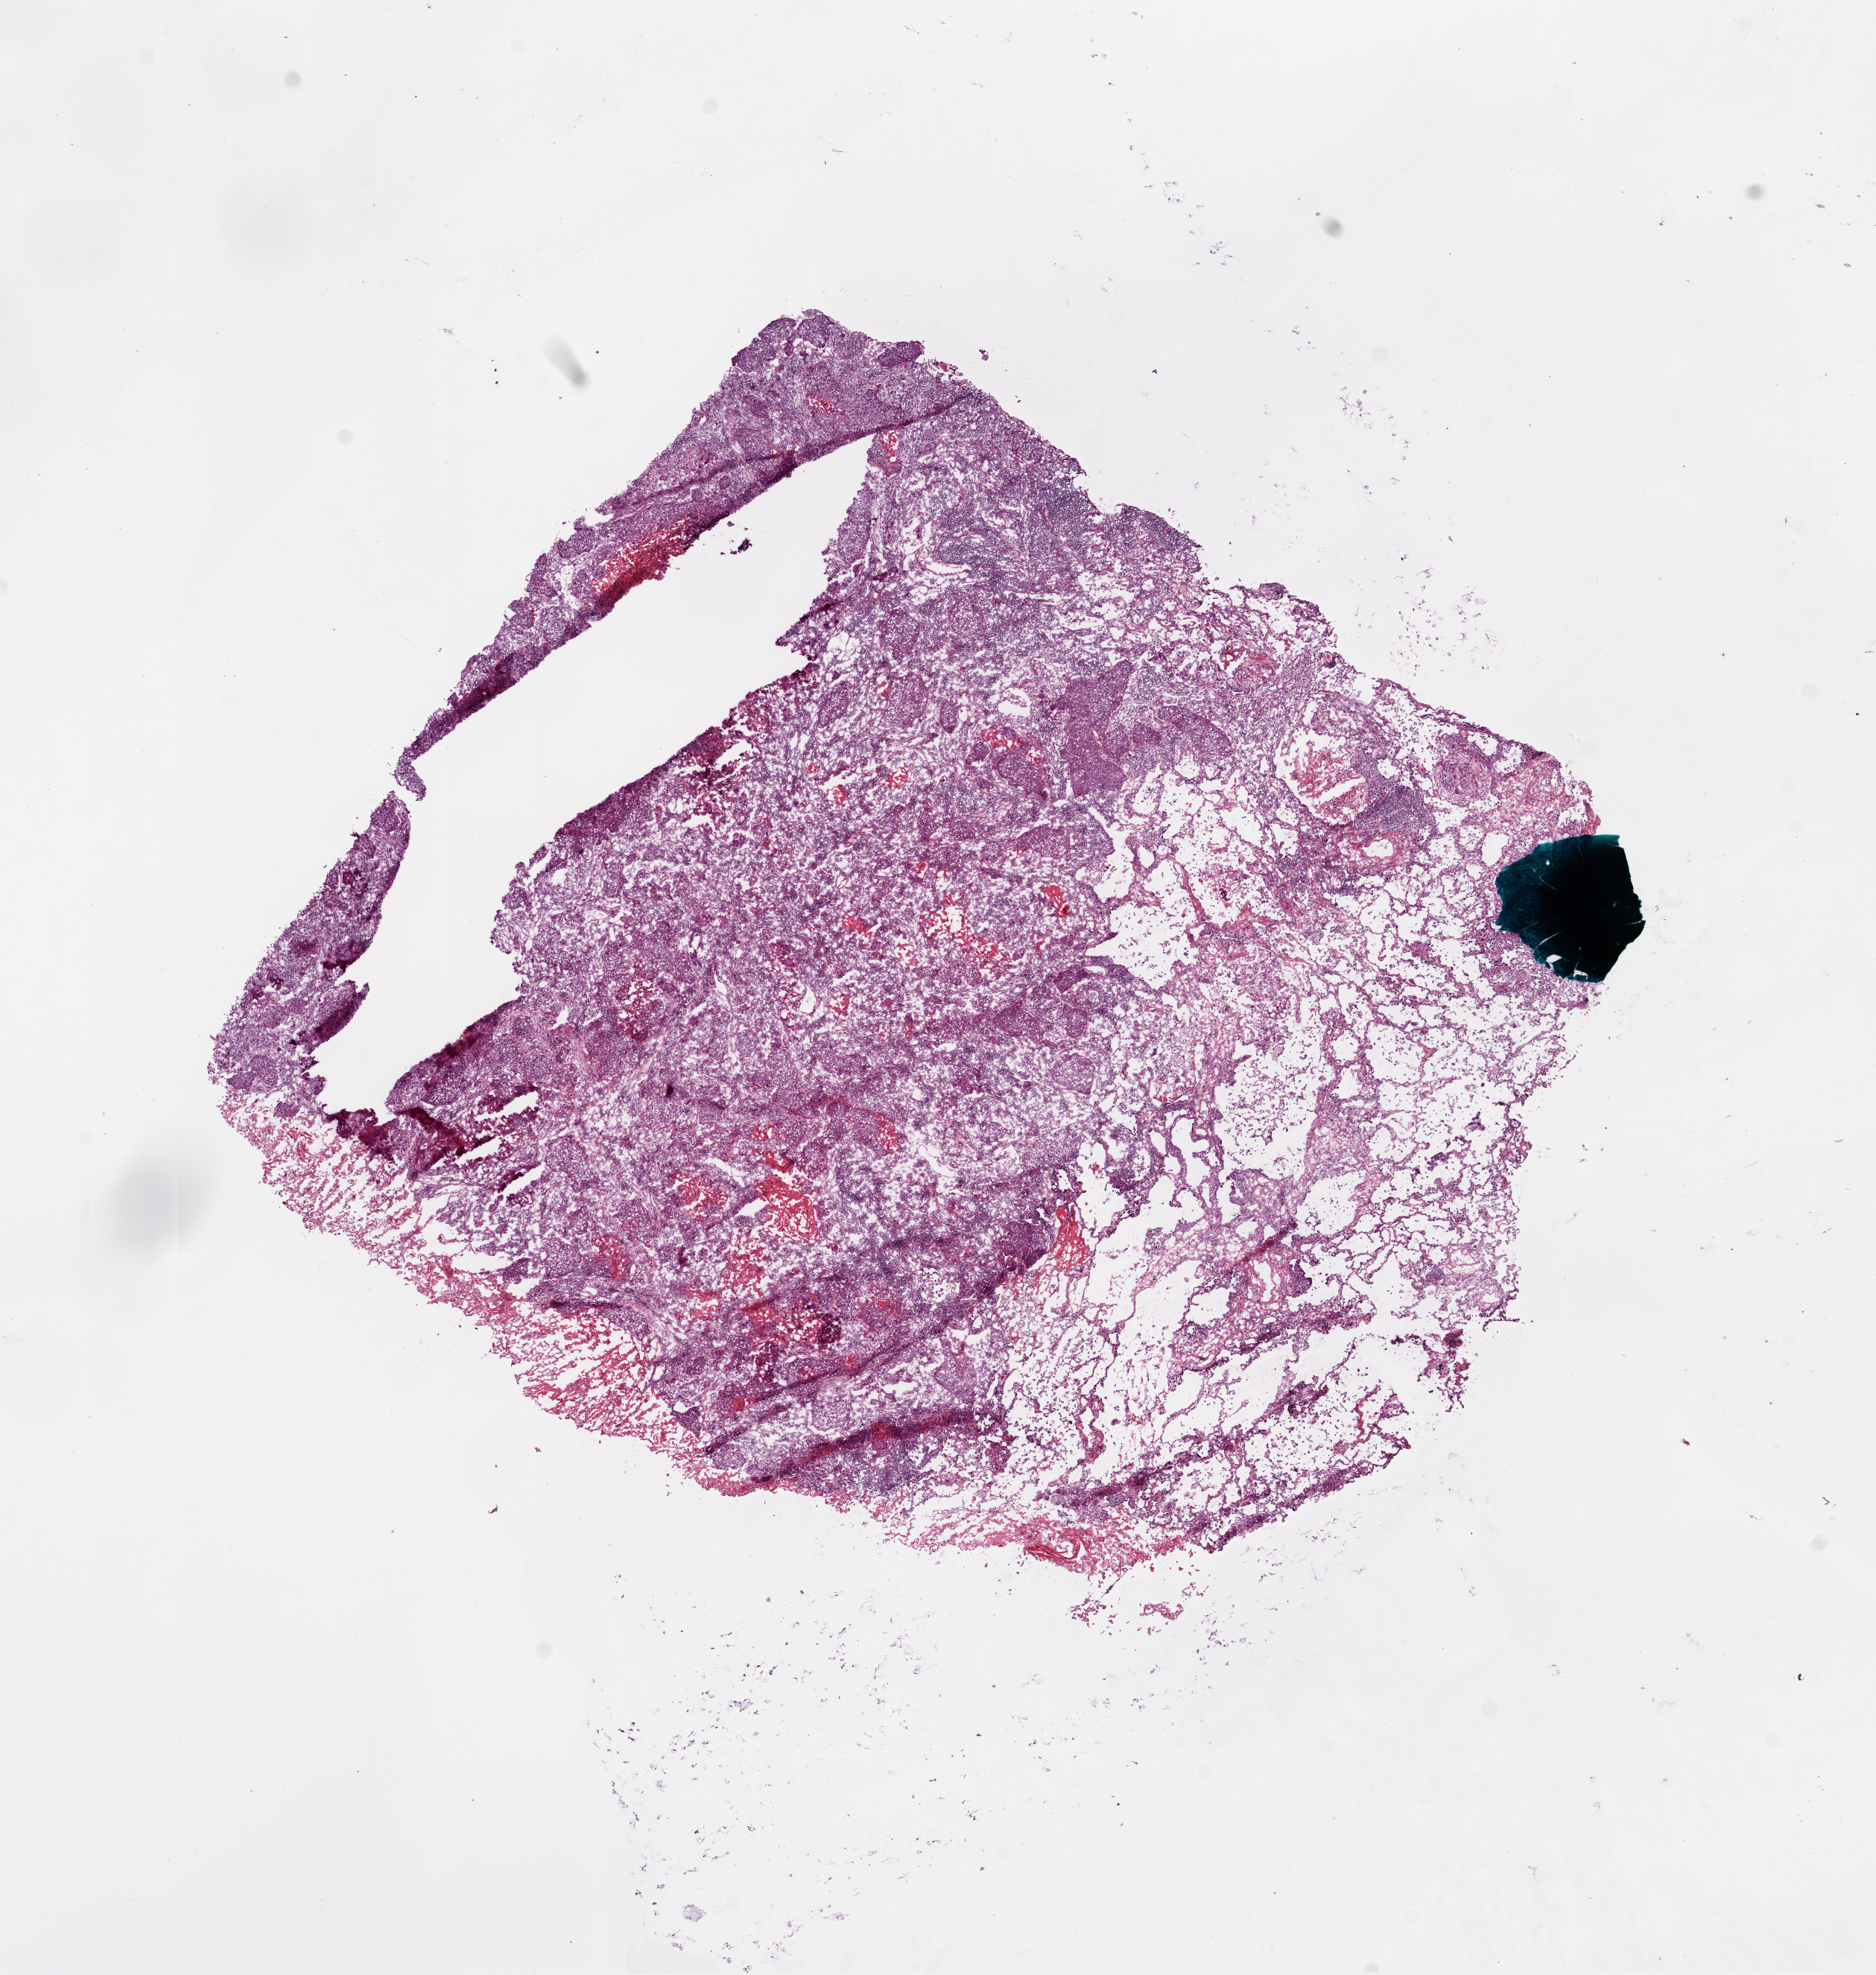
H&E-stained whole-slide image, a low-resolution overview of the entire scanned area, about 10.2 x 10.7 mm, frozen section from the bottom of the tissue portion, lung, primary tumour sample. Patient: female, age at initial diagnosis 54 years.
Diagnosis: Squamous cell carcinoma, NOS (lower lobe, lung).